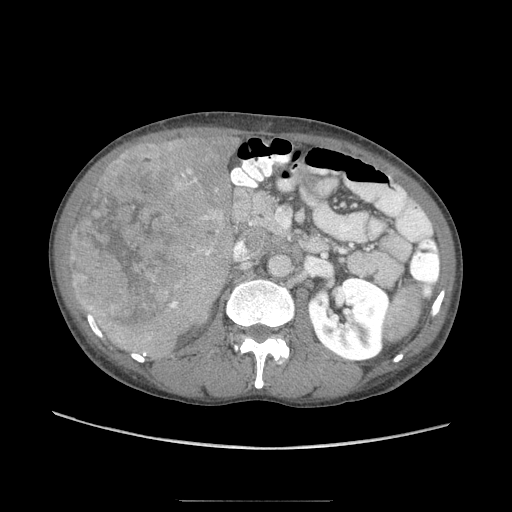
Contrast-enhanced abdominal CT (liver protocol), one axial slice; slice 31 of 103 in the series (ordered by position); 120 kVp; soft-tissue window (W 400 / L 40 HU); 2.5 mm slice thickness; 512 × 512 image matrix. From the clinical record (not read from this slice): diagnosis: hepatocellular carcinoma (patient treated with transarterial chemoembolisation; whether this scan precedes or follows treatment is not stated here); TNM stage (as recorded): Stage-IIIA; Child-Pugh class: A; tumour size: 16 cm.
Structures marked on this image (semi-automatic segmentation, software-assisted and operator-edited):
- liver parenchyma outside the tumour (the mass and vessels are separate outlines, so this box may not span the whole liver): bounding box (x1, y1, x2, y2) in pixels: (72, 135, 238, 351)
- mass: (66, 141, 220, 344)